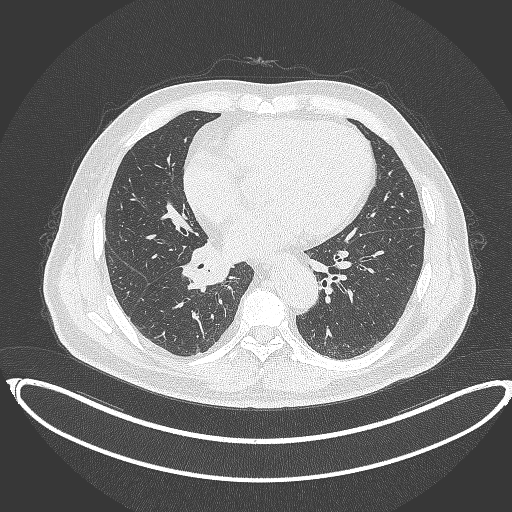
Chest CT, one axial slice. Slice 176 of 387 in the series (ordered by position). Lung window (W 1500 / L -600 HU). 512 × 512 image matrix, field of view 448 × 448 mm. Male patient, age 61 years. From the clinical record (not read from this slice): clinical TNM (as recorded): T1b N1 M0.
Structures marked on this image (rectangle marked by the reading radiologist):
- lung tumour (recorded histology: squamous cell carcinoma): bounding box <180,241,233,294> (left, top, right, bottom; pixels)